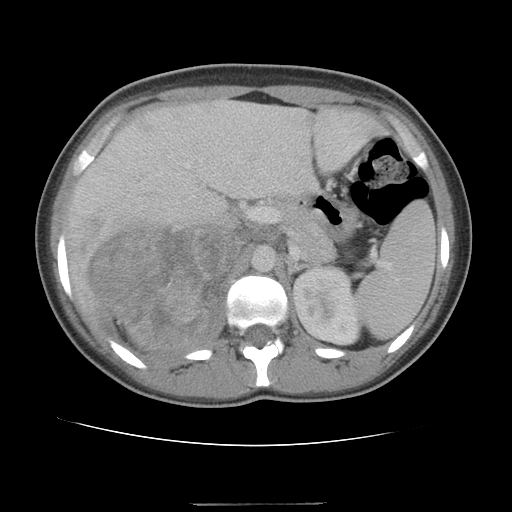
Contrast-enhanced abdominal CT, one axial slice. Slice 72 of 100 in the series (ordered by position). 120 kVp. Intravenous contrast given. Soft-tissue window (W 400 / L 40 HU). 5 mm slice thickness. 512 × 512 image matrix, field of view 360 × 360 mm. Female patient, age 21 years. From the clinical record (not read from this slice): diagnosis: adrenocortical carcinoma; tumour side: right adrenal; tumour size at pathology: 15.5 cm; Ki-67 index: 26 %; stage (as recorded): 3.
Structures marked on this image (semi-automatic segmentation, software-assisted and operator-edited):
- mass: bounding box (x1, y1, x2, y2) in pixels: (93, 228, 230, 354)